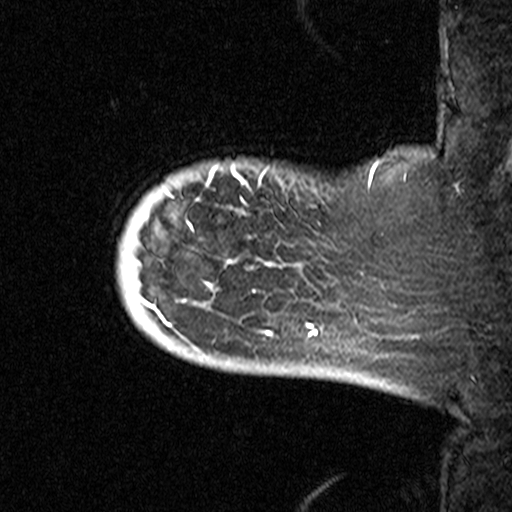
Breast MRI (dynamic contrast-enhanced), one sagittal slice. Position 5 of 44 along the scan axis. Dynamic contrast-enhanced study with each time point stored as its own series, time point 2 of 3 at this slice position (early post-contrast, ordered by acquisition time). 1.5 T. TE 4.5 ms, TR 11 ms. 3.27 mm slice thickness. 512 × 512 image matrix, field of view 200 × 200 mm. Female patient, age 53 years. From the clinical record (not read from this slice): setting: breast cancer imaged before/during neoadjuvant chemotherapy; receptor status: HR-positive, HER2-negative.
Annotated regions visible in this slice (semi-automatically segmented with operator editing):
- analysis volume of interest (the breast-tissue region the enhancement analysis was run in; not a lesion): bounding box <107,154,311,367> (left, top, right, bottom; pixels)
- tumour enhancement mask (voxels above the 90 % enhancement threshold inside the analysis volume of interest): <144,166,272,335>